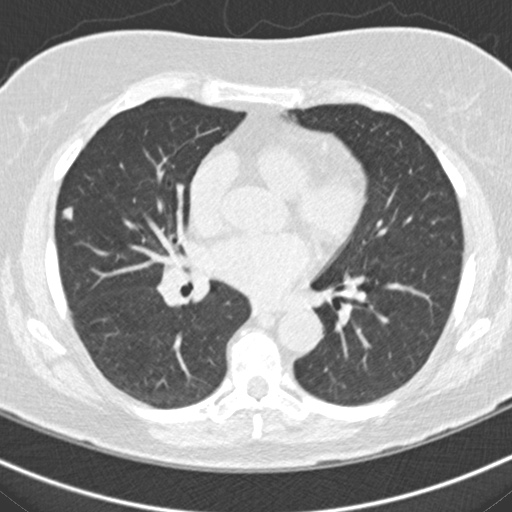
Low-dose screening chest CT, one axial slice; position 96 of 160 along the scan axis; reconstruction kernel B30f; 120 kVp; lung window (W 1500 / L -600 HU); 512 × 512 image matrix, field of view 316 × 316 mm.
Outlined on this slice (expert manual segmentation):
- lesion 1 (tumor, middle lobe of right lung): bounding box [x1, y1, x2, y2] px = [63, 208, 72, 219]